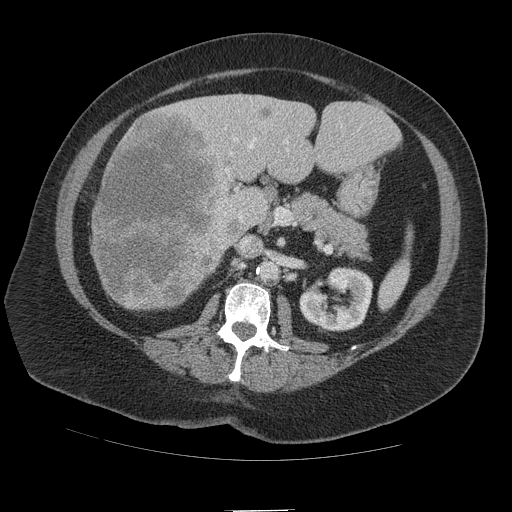
Contrast-enhanced abdominal CT (liver protocol), one axial slice; position 49 of 109 along the scan axis; 140 kVp; soft-tissue window (W 400 / L 40 HU); 2.5 mm slice thickness; 512 × 512 image matrix. Case-level facts recorded for this patient, not image findings: diagnosis: hepatocellular carcinoma (patient treated with transarterial chemoembolisation; whether this scan precedes or follows treatment is not stated here); TNM stage (as recorded): Stage-IVB; Child-Pugh class: A; tumour nodularity: multinodular.
Annotated regions visible in this slice (semi-automatically segmented with operator editing):
- liver parenchyma outside the tumour (the mass and vessels are separate outlines, so this box may not span the whole liver): bounding box <92,94,400,310> (left, top, right, bottom; pixels)
- mass: <90,106,242,311>
- liver vessels: <225,99,289,221>